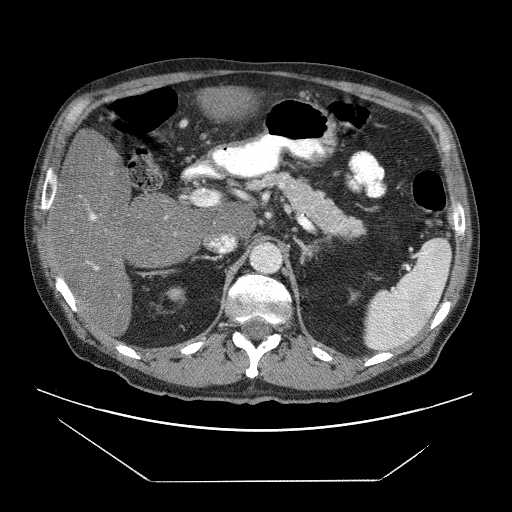
Contrast-enhanced abdominal CT (liver protocol), one axial slice. Slice 32 of 83 in the series (ordered by position). Reconstruction kernel STANDARD. 120 kVp. Soft-tissue window (W 400 / L 40 HU). 512 × 512 image matrix, field of view 420 × 420 mm. From the clinical record (not read from this slice): diagnosis: hepatocellular carcinoma (patient treated with transarterial chemoembolisation; whether this scan precedes or follows treatment is not stated here); TNM stage (as recorded): Stage-IVB; Child-Pugh class: B; tumour differentiation: poorly differentiated.
Structures marked on this image (semi-automatic segmentation, software-assisted and operator-edited):
- liver parenchyma outside the tumour (the mass and vessels are separate outlines, so this box may not span the whole liver): bounding box <46,86,258,314> (left, top, right, bottom; pixels)
- liver vessels: <51,188,168,270>